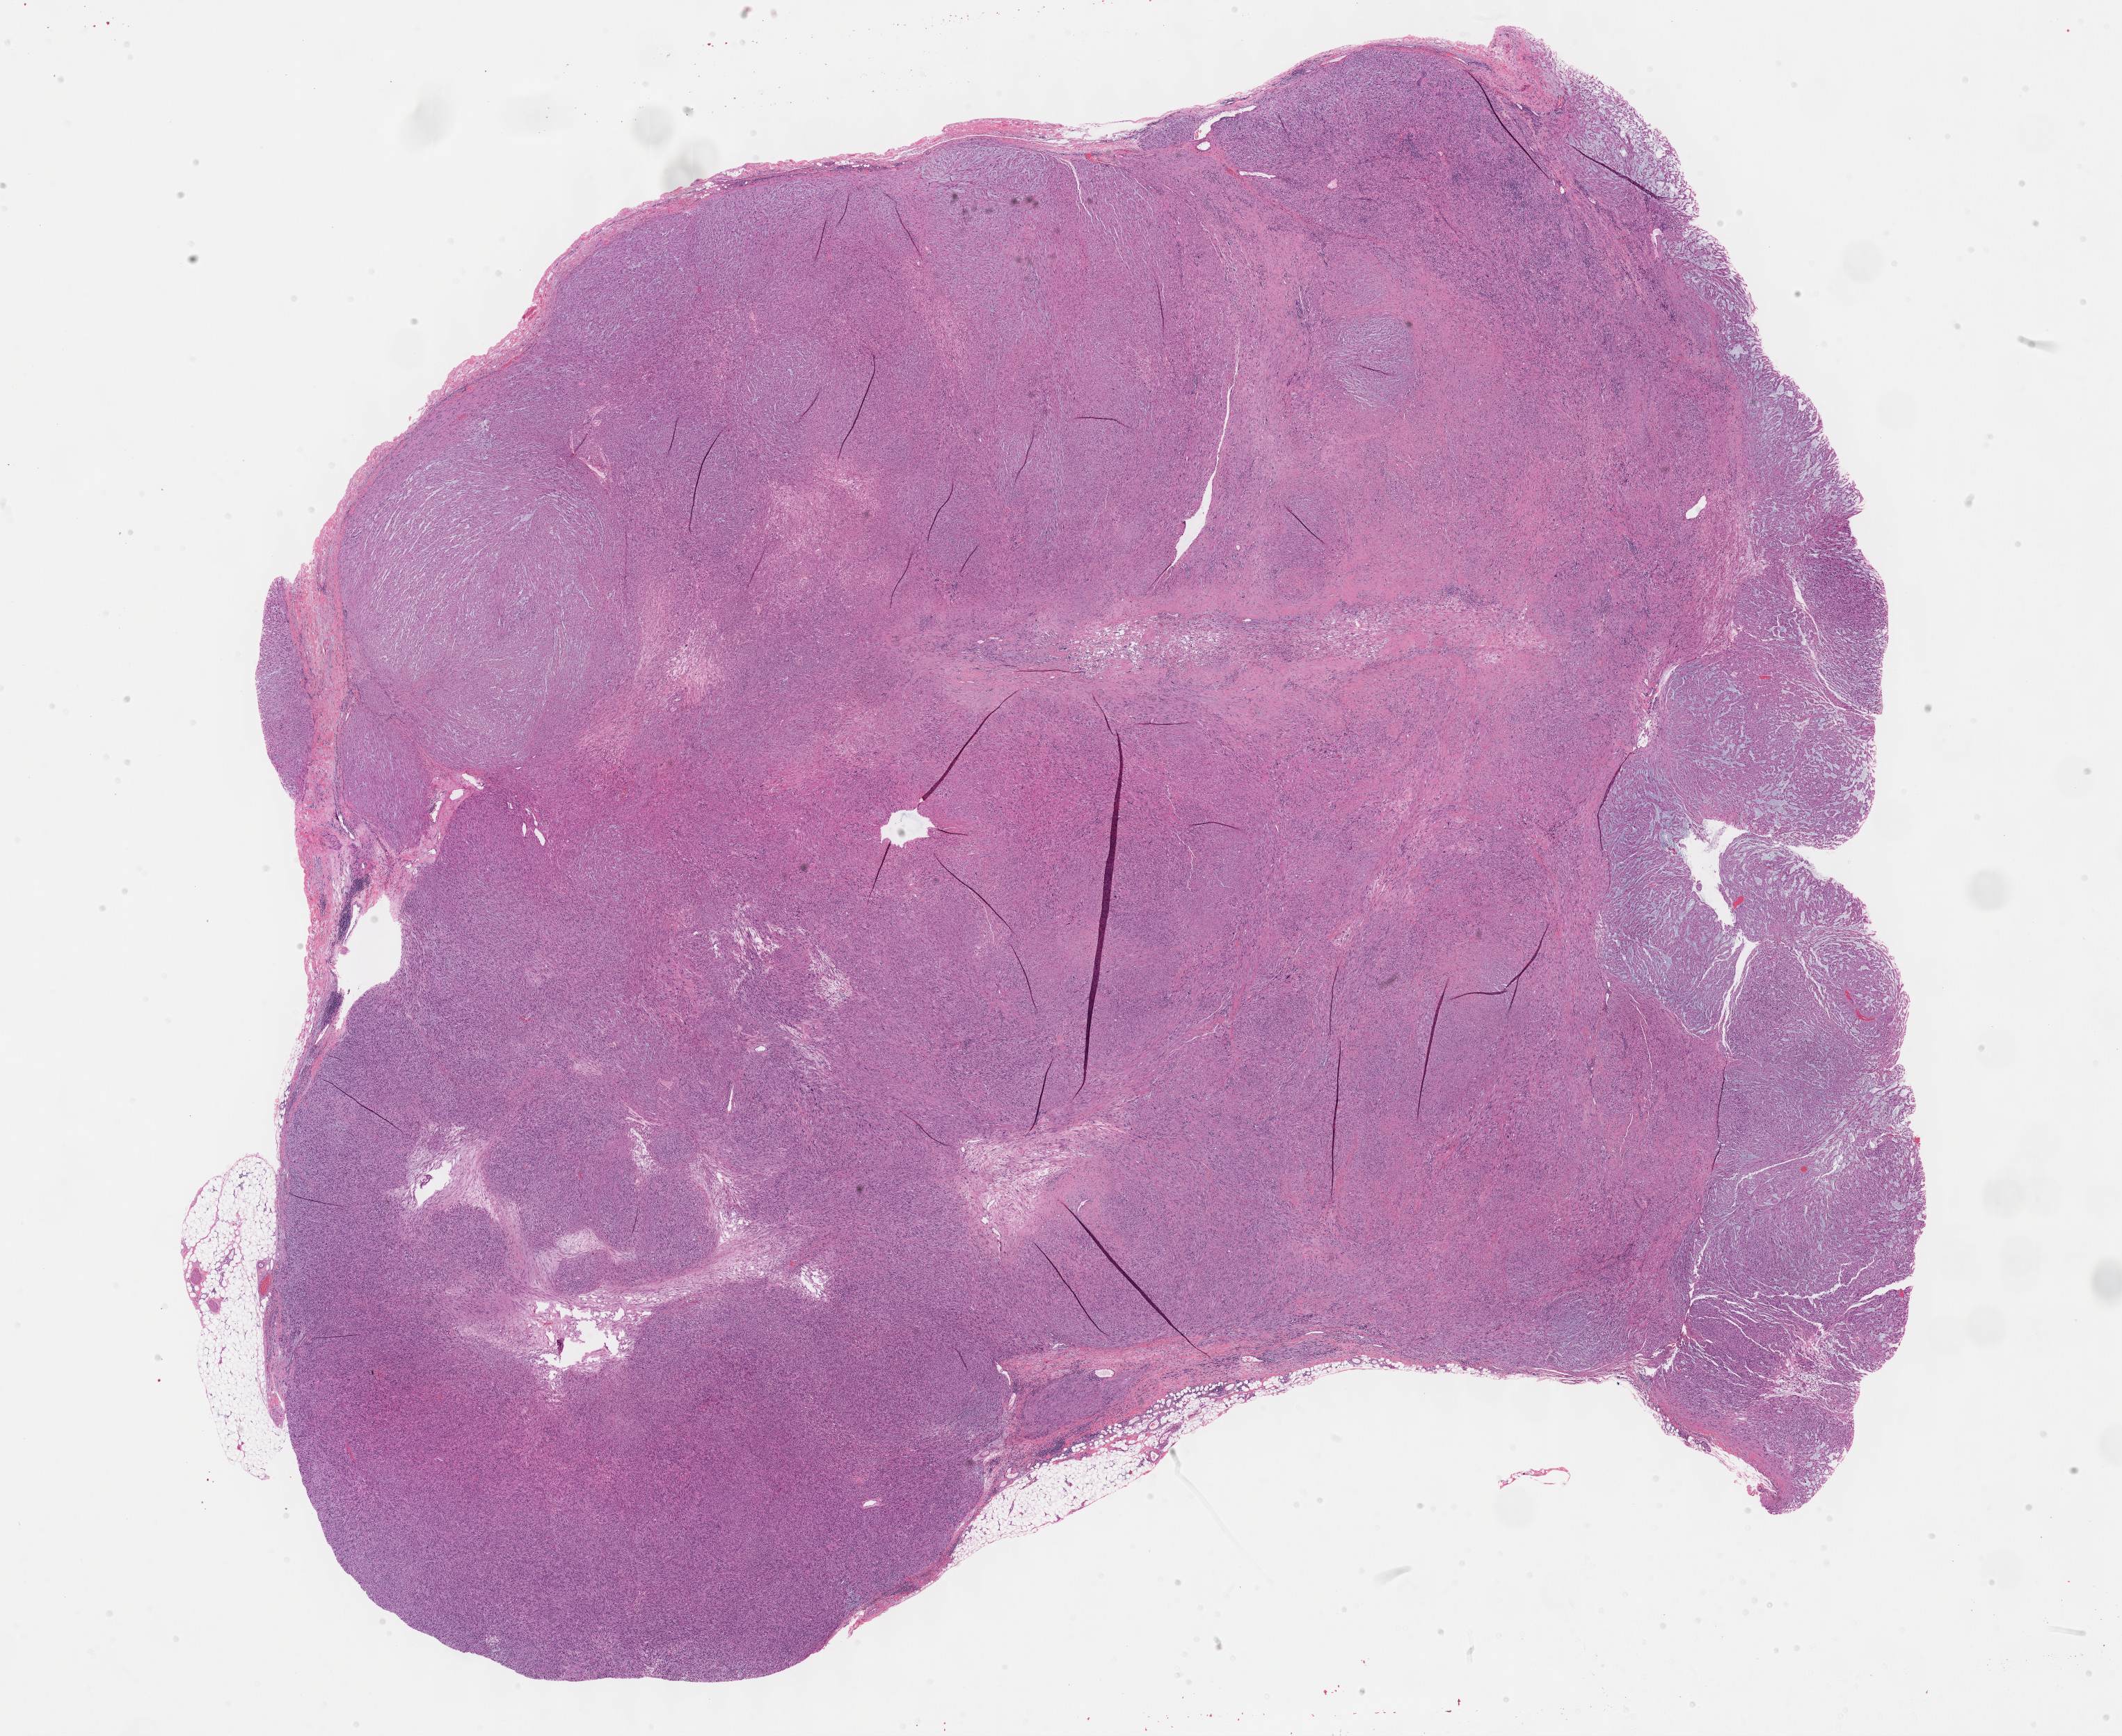
H&E-stained whole-slide image, whole scanned area (about 24.7 x 20.2 mm) shown as a low-resolution overview, formalin-fixed paraffin-embedded (FFPE) diagnostic section, sample: primary tumour, connective, subcutaneous and other soft tissues. Female patient; age at initial diagnosis 82 years.
* histologic diagnosis: Leiomyosarcoma, NOS (connective, subcutaneous and other soft tissues of lower limb and hip)